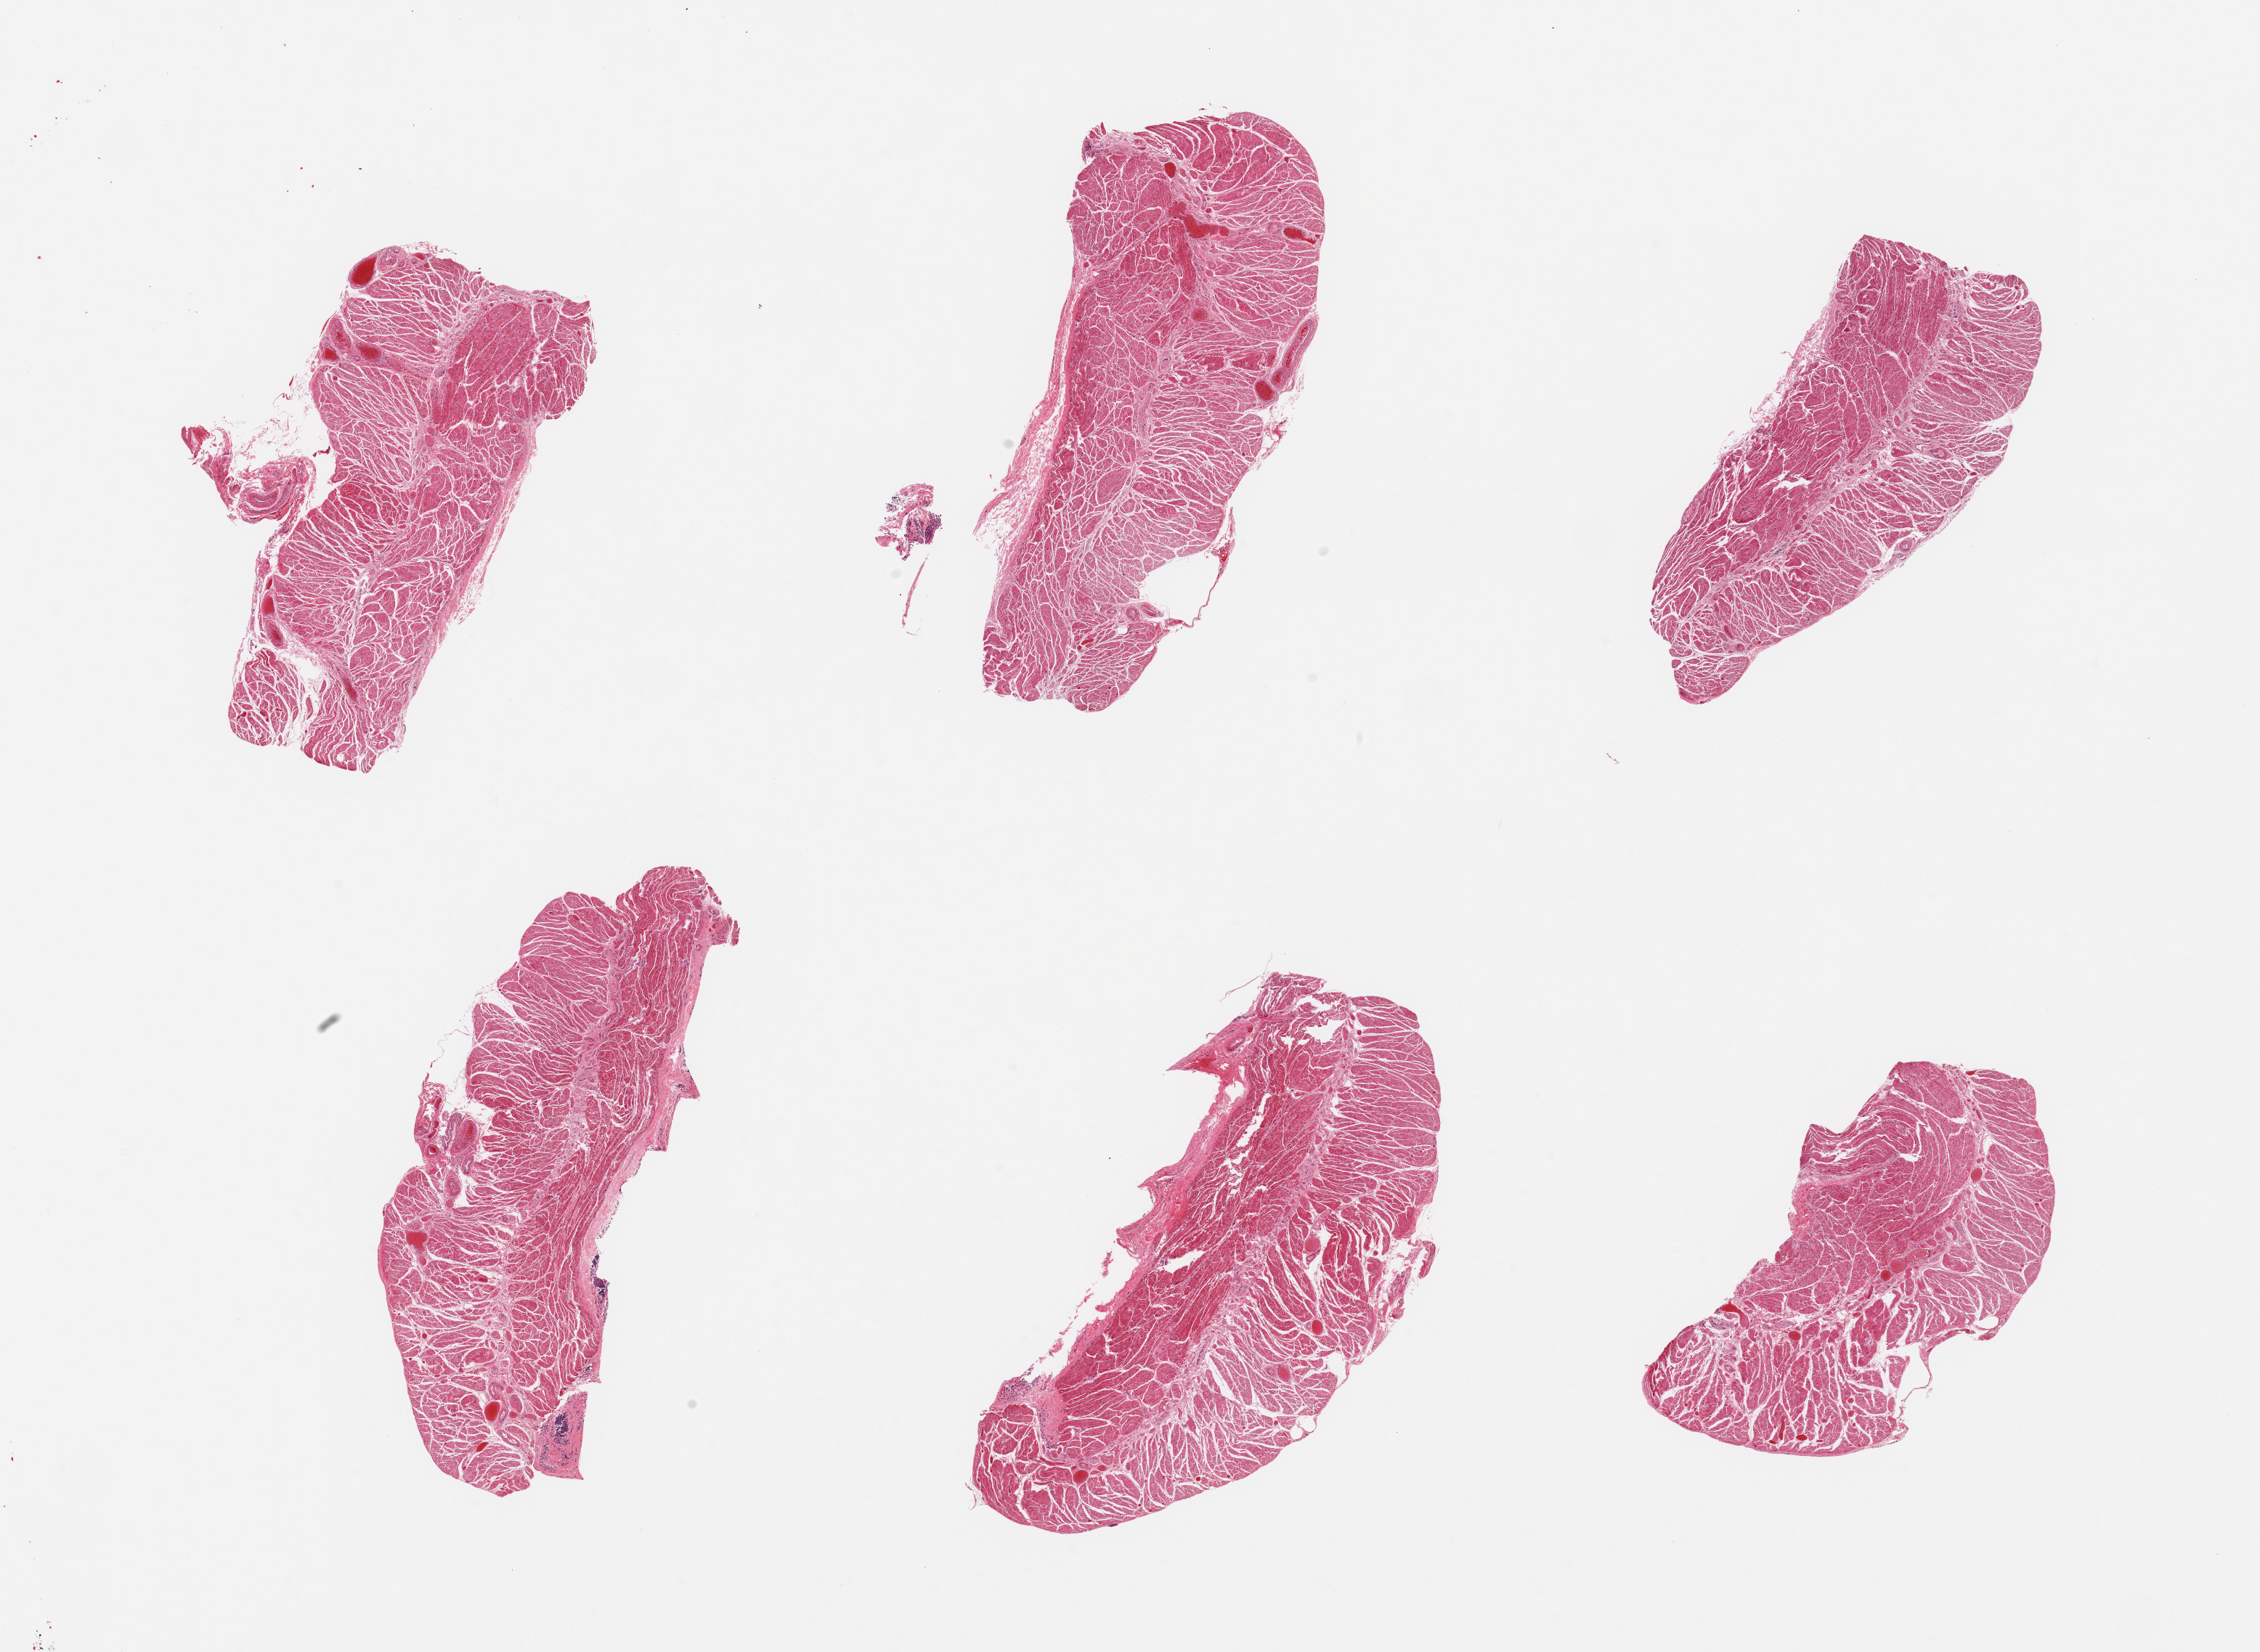
H&E whole-slide image — a low-resolution overview of the entire scanned area, about 24.6 x 18.0 mm (from a 20x scan); PAXgene-fixed paraffin-embedded (PFPE) section; target tissue: gastroesophageal junction; tissue donor sample. Donor sex: female.
* pathologist's review note for this sample: 6 pieces, confirmed target muscularis